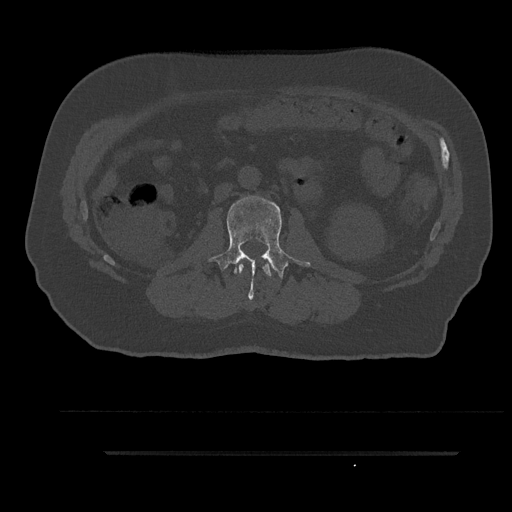
CT including the spine, one axial slice. Position 113 of 797 along the scan axis. Reconstruction kernel Br40s/3. Bone window (W 1800 / L 400 HU). 512 × 512 image matrix, field of view 432 × 432 mm. Male patient, age 63 years. Case-level facts recorded for this patient, not image findings: primary cancer: renal.
Annotated regions visible in this slice (semi-automatically segmented with operator editing):
- L1 vertebra: bounding box (x1, y1, x2, y2) in pixels: (238, 263, 272, 276)
- L2 vertebra: (208, 196, 310, 299)